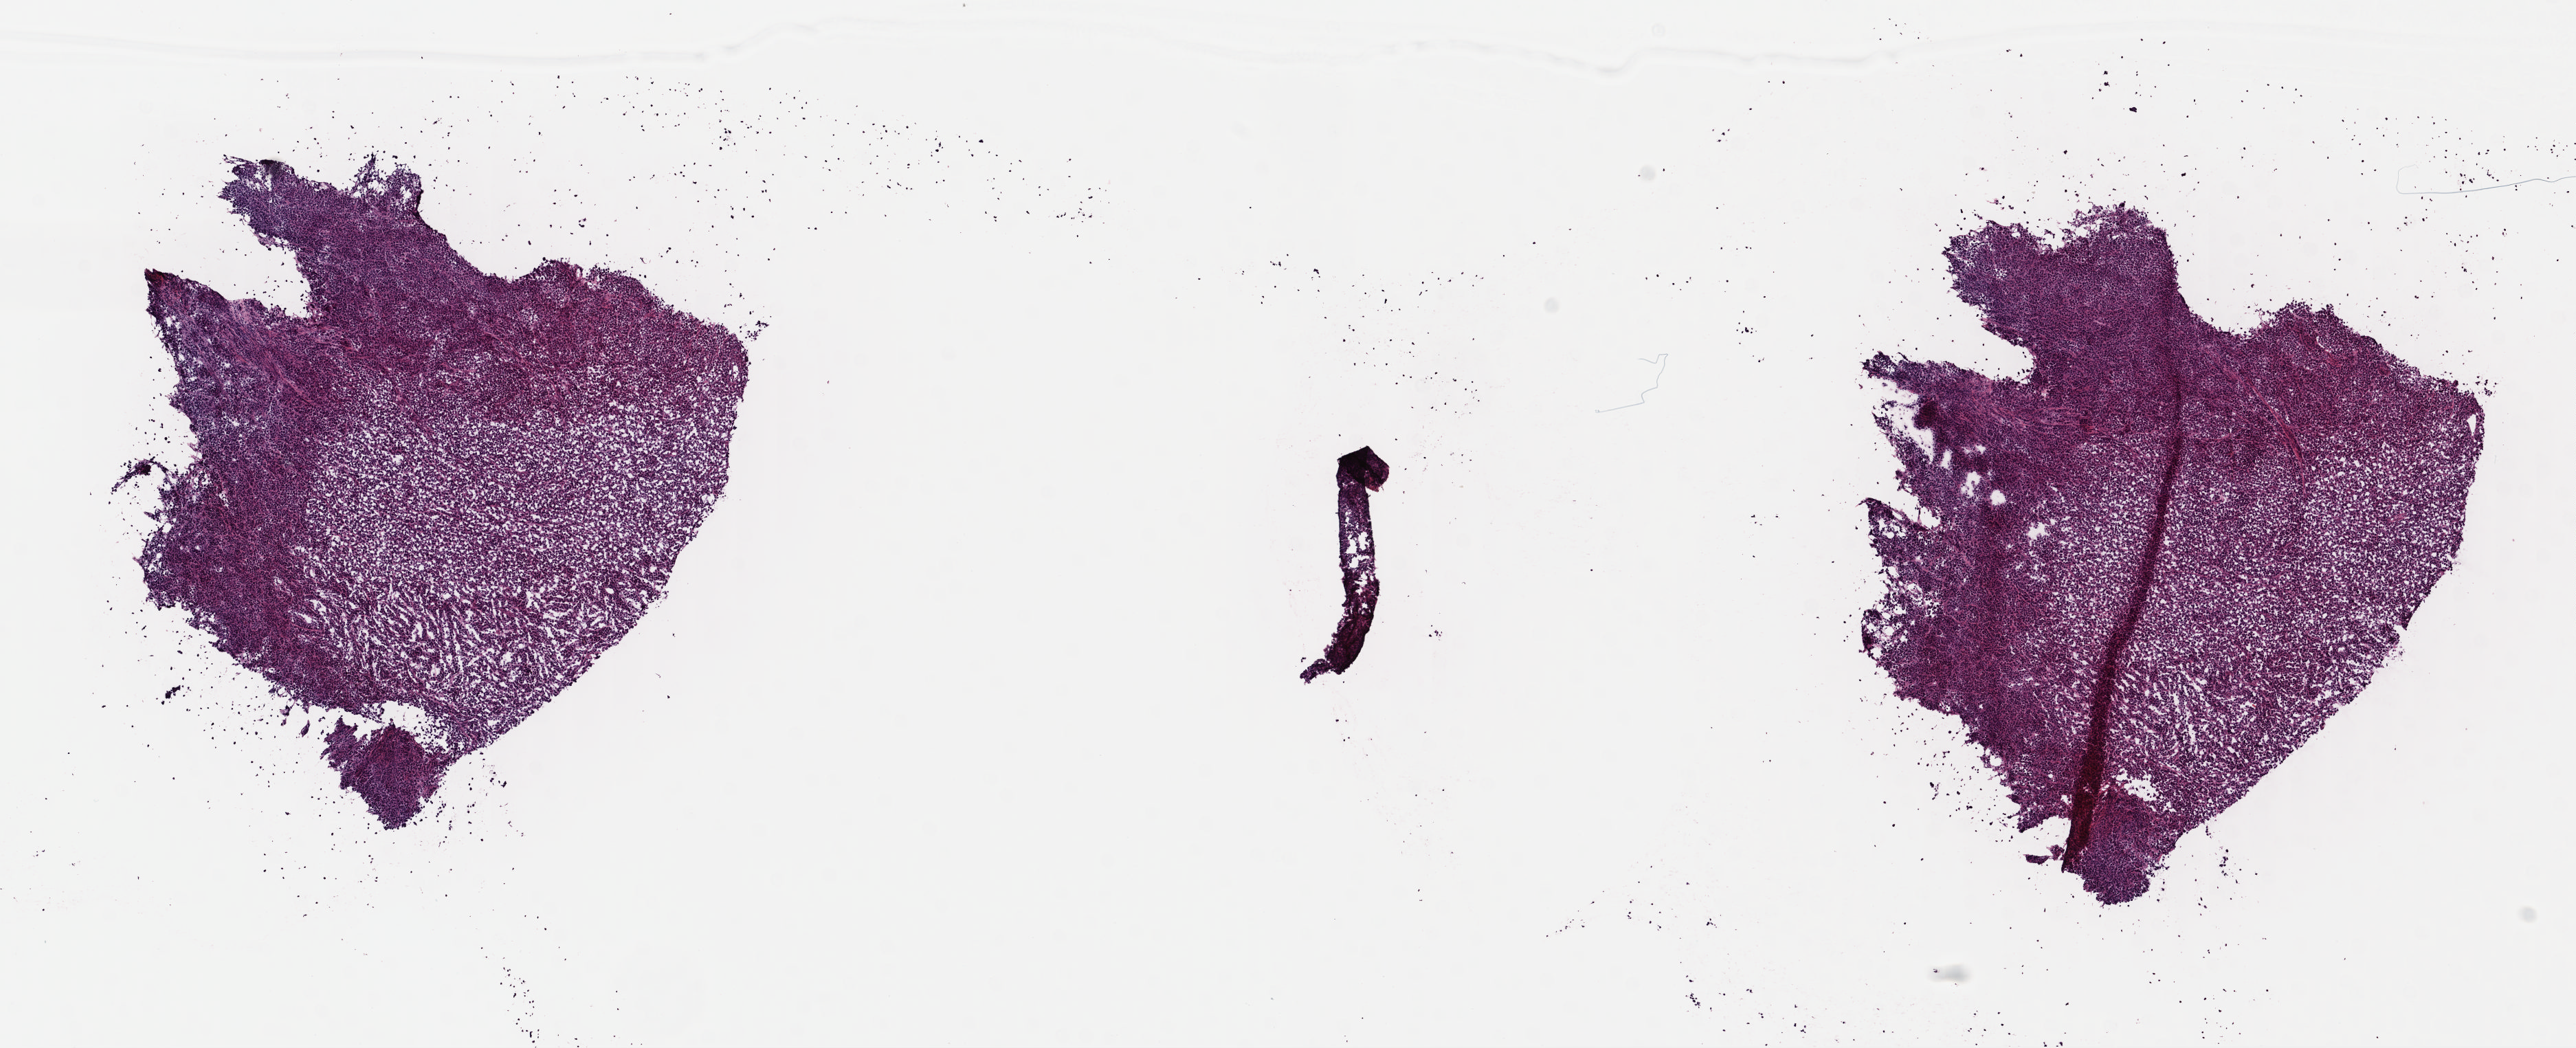
Whole-slide histology image, H&E, low-resolution overview of the scanned area, about 14.7 x 6.0 mm; frozen section; metastatic tumour sample. Male patient; age at initial diagnosis 58 years. Slide review estimates, as recorded: tumour cells 90%, tumour nuclei 90%, normal cells 0%, stromal cells 10%, necrosis 0%. Infiltration values recorded for this section: lymphocyte infiltration 2%, monocyte infiltration 0%, neutrophil infiltration 0%.
This section: metastatic tumour tissue. Patient diagnosis: Malignant melanoma, NOS.